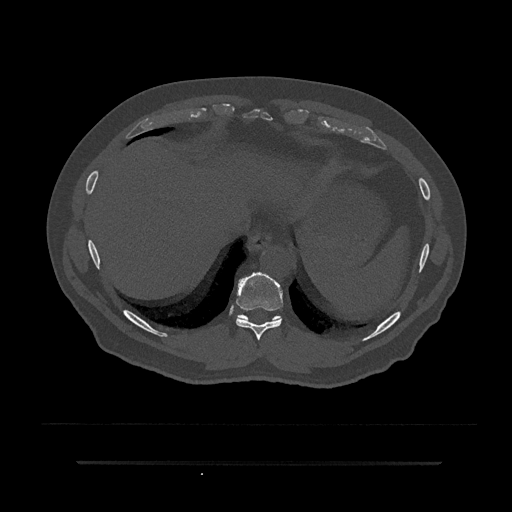
CT including the spine, one axial slice; slice 364 of 797 in the series (ordered by position); reconstruction kernel Br40s/3; bone window (W 1800 / L 400 HU); 0.5 mm slice thickness; 512 × 512 image matrix, field of view 464 × 464 mm. Male patient, age 59 years. Case-level facts recorded for this patient, not image findings: primary cancer: bile ducts; vertebrae with lytic lesions (as recorded): T10.
Annotated regions visible in this slice (semi-automatically segmented with operator editing):
- T10 vertebra: bounding box [x1, y1, x2, y2] px = [238, 314, 279, 324]
- T9 vertebra: [236, 272, 284, 340]